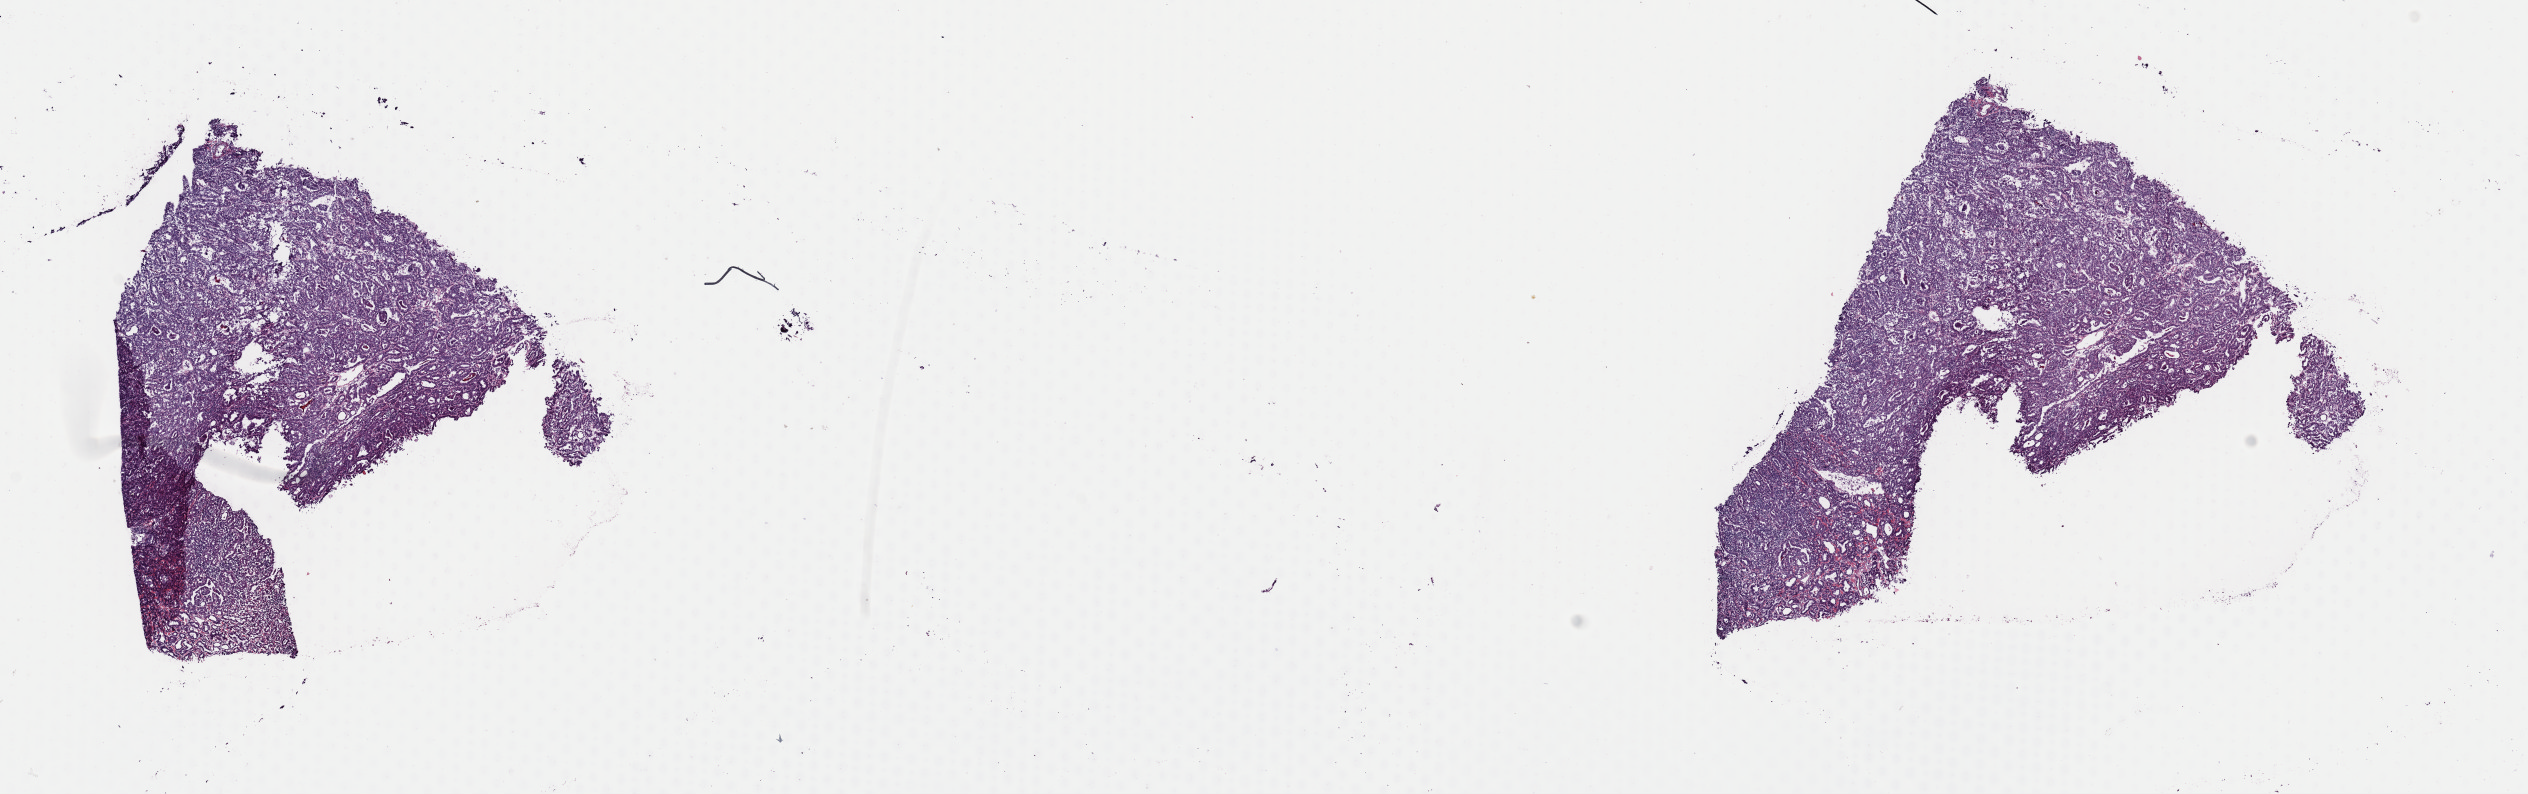
Digitized Hematoxylin and eosin (H&E) stained tissue section (whole slide), low-resolution overview of the scanned area, about 20.0 x 6.3 mm (from a 40x scan). Frozen section. Primary tumour sample from the thyroid. Female, age 55 years at initial diagnosis. Composition of this section per pathologist review: tumour cells 95%, tumour nuclei 95%, normal cells 0%, stromal cells 5%, necrosis 0%. Infiltration values recorded for this section: lymphocyte infiltration 0%, monocyte infiltration 0%, neutrophil infiltration 0%.
- laterality: right
- AJCC pathologic stage: I (7th edition)
- pathologic diagnosis: Papillary carcinoma, follicular variant (thyroid gland)
- lymph nodes positive (case pathology): 0 of 13 examined
- TNM: T1 N0 M0